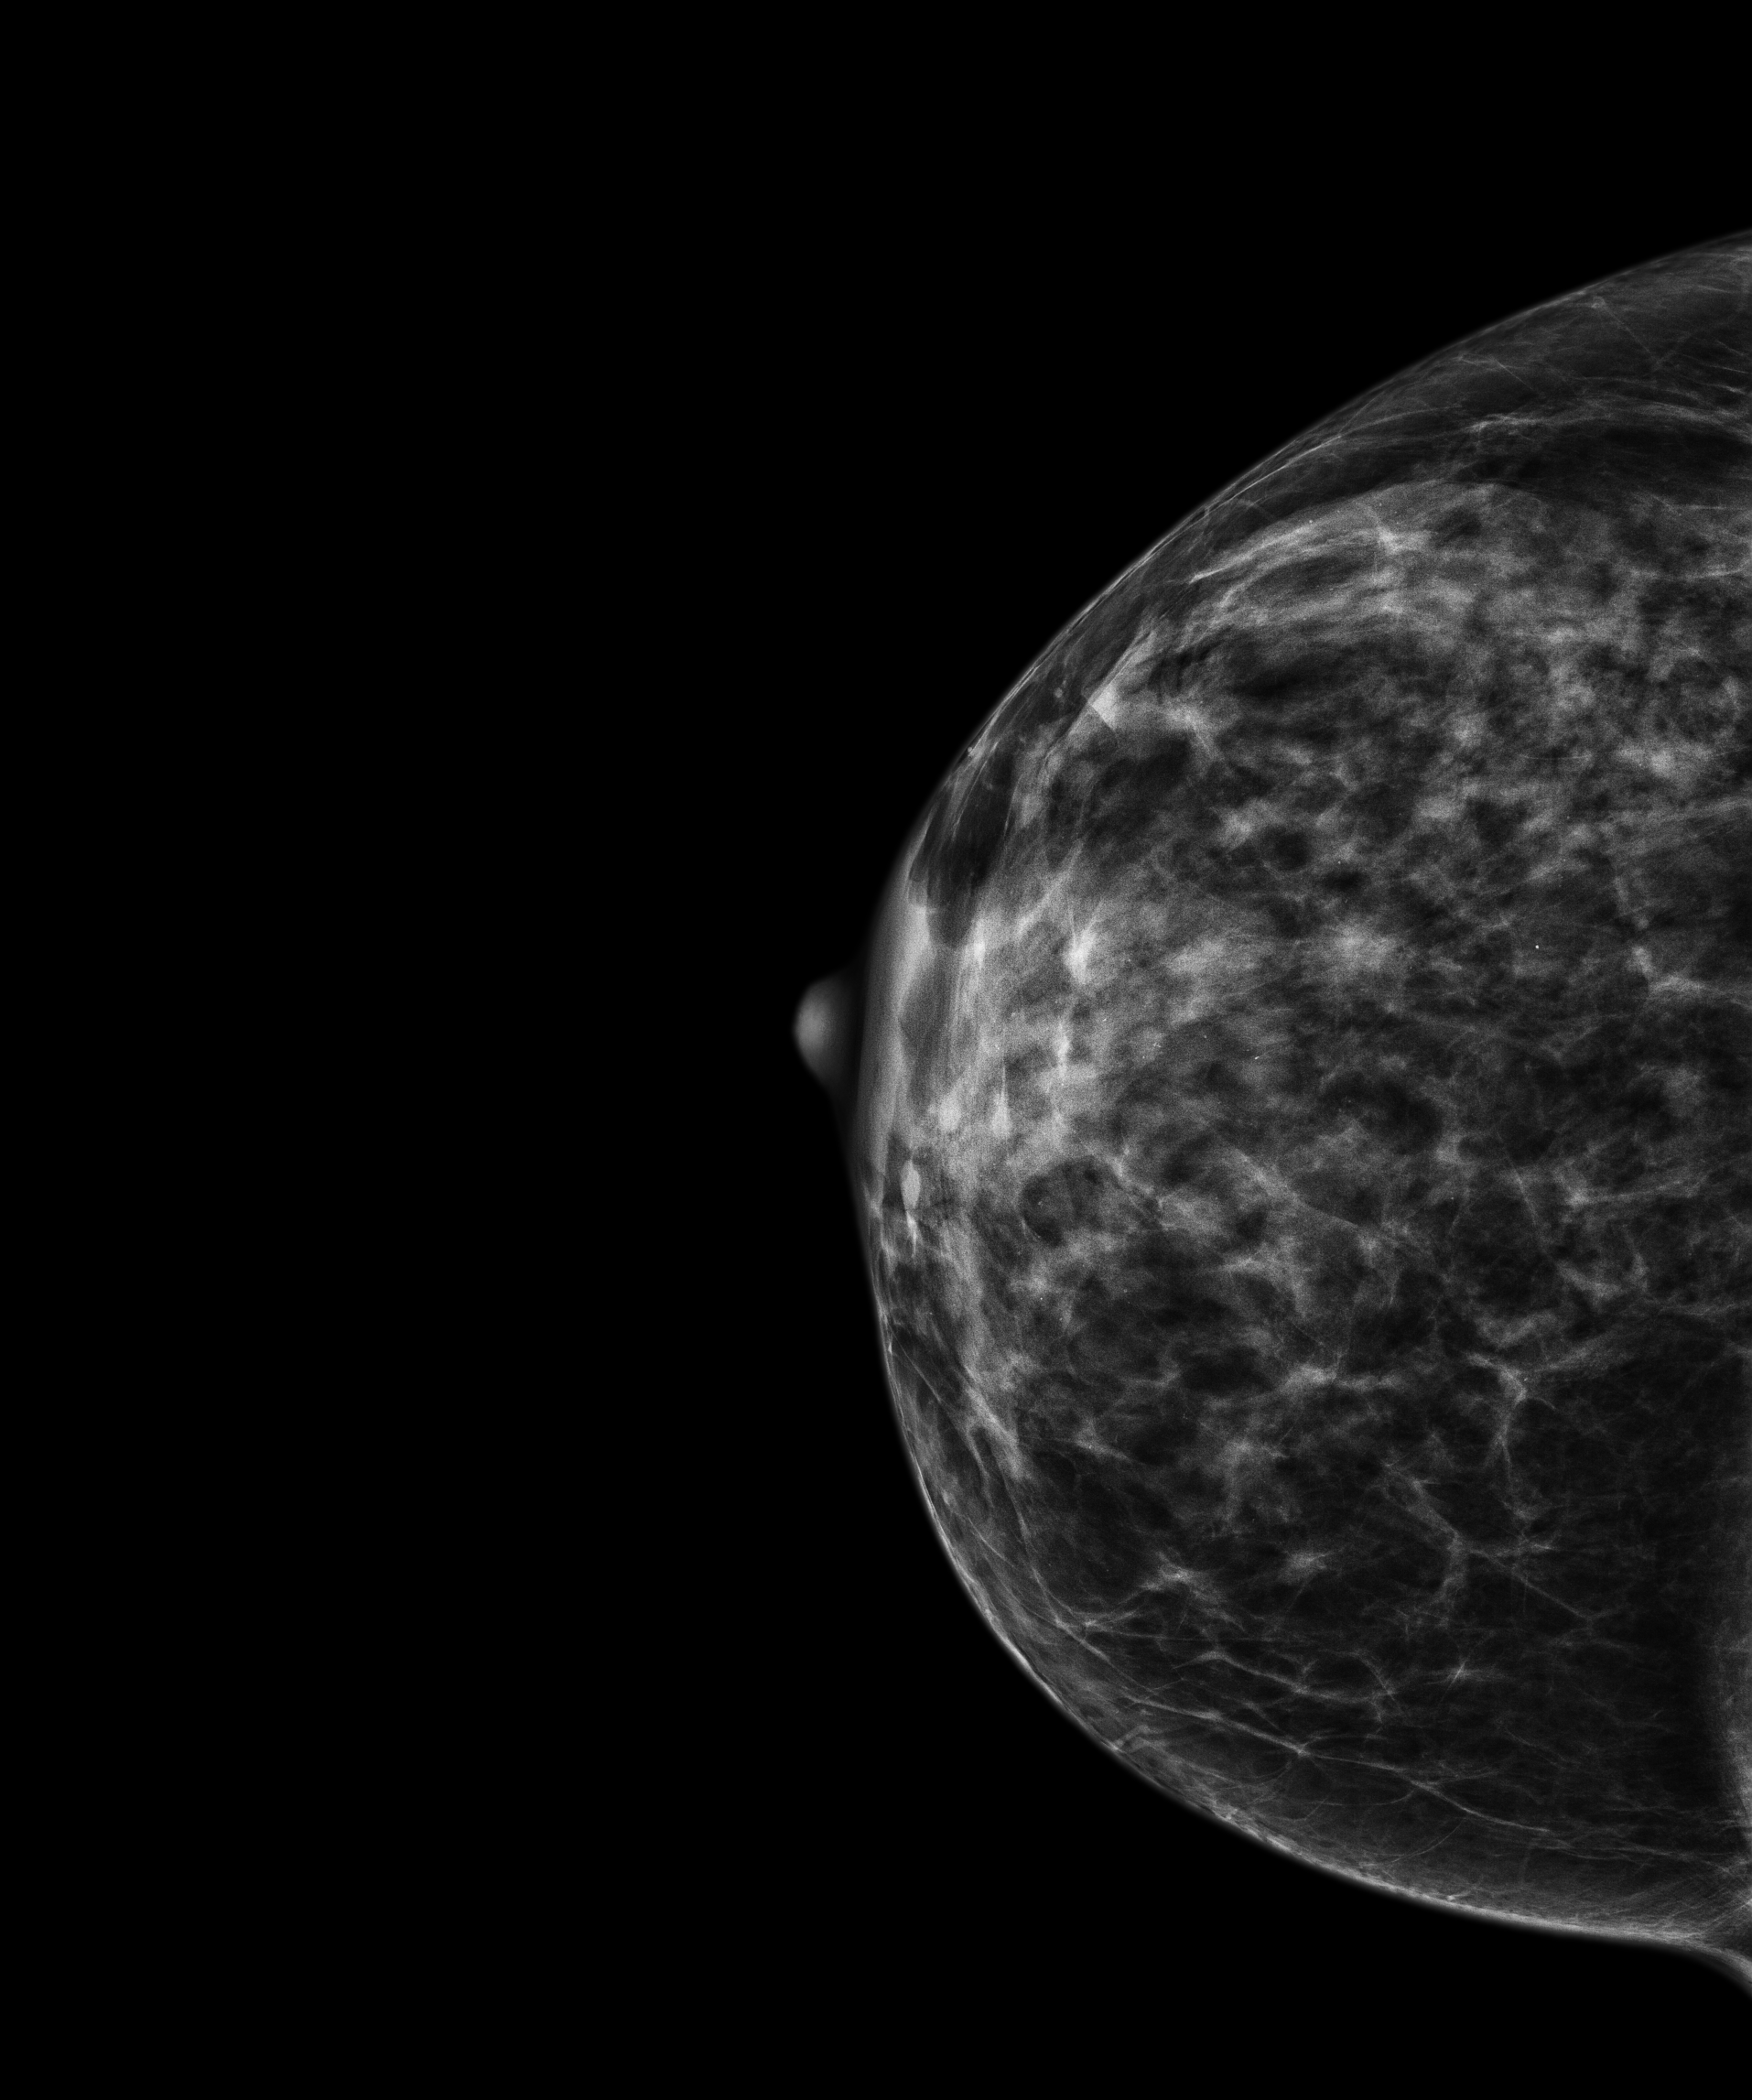
Screening examination. Female patient, age 48 years.
Image type: full-field digital mammogram. Breast: right. Projection: cranio-caudal projection.